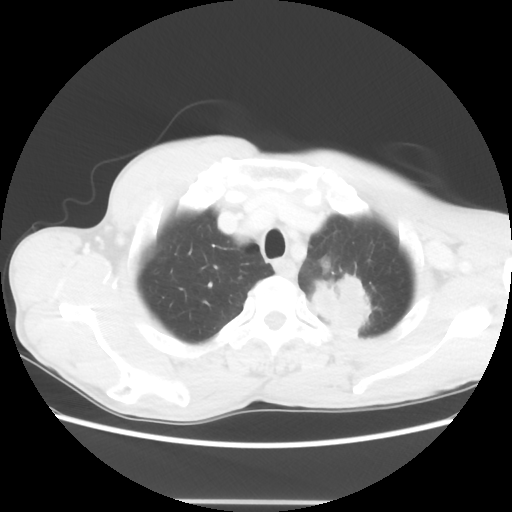
Chest CT, one axial slice; position 56 of 62 along the scan axis; 100 kVp; lung window (W 1500 / L -600 HU); 512 × 512 image matrix, field of view 360 × 360 mm. Male patient, age 61 years. Case-level facts recorded for this patient, not image findings: clinical TNM (as recorded): T3 N1 M1.
Structures marked on this image (rectangle marked by the reading radiologist):
- lung tumour (recorded histology: adenocarcinoma): bounding box [x1, y1, x2, y2] px = [314, 265, 372, 342]